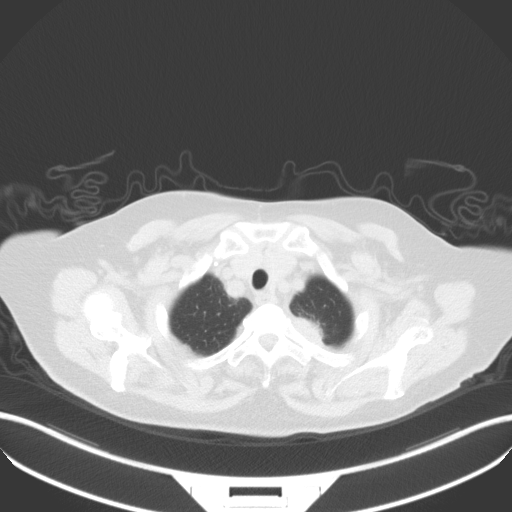
Chest CT, one axial slice; slice 44 of 50 in the series (ordered by position); 100 kVp; lung window (W 1500 / L -600 HU); 5 mm slice thickness; 512 × 512 image matrix. Patient: female, 81 years. Case-level facts recorded for this patient, not image findings: clinical TNM (as recorded): T2a N0 M0.
Annotated regions visible in this slice (rectangle marked by the reading radiologist):
- lung tumour (recorded histology: adenocarcinoma): bounding box (x1, y1, x2, y2) in pixels: (284, 309, 330, 352)